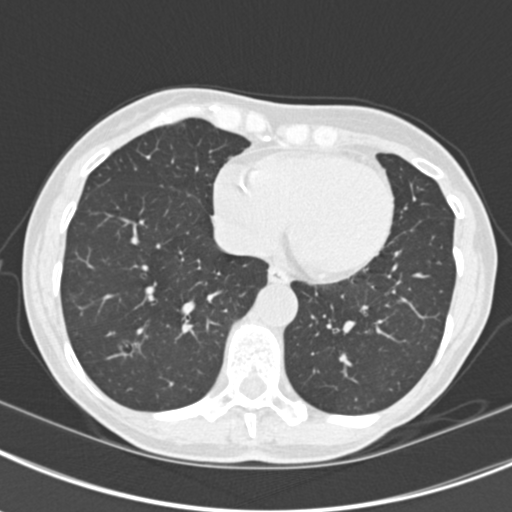
Axial slice from a low-dose chest CT screening exam; second annual screen; lung window (W 1500 / L -600 HU); 2 mm slice thickness; standard (soft-tissue) reconstruction kernel (B30f); 512 × 512 image matrix, field of view 298 × 298 mm. Female participant, aged 63 years at enrolment. Current smoker at enrolment.
Expert-annotated lung lesion, bounding box [x1, y1, x2, y2] px = [109, 327, 152, 369]. The screening reader recorded 9 non-calcified nodules or masses ≥4 mm on this exam (left upper lobe, right upper lobe, left upper lobe, left lower lobe, right middle lobe, left lower lobe, left lower lobe, right lower lobe, right lower lobe); which of them this box marks is not recorded. Official screen result: positive, other. Lung cancer was diagnosed 408 days after this screen (after the third annual screen): bronchiolo-alveolar adenocarcinoma, NOS, right upper lobe, right middle lobe, right lower lobe, left upper lobe, left lower lobe, moderately differentiated (G2), stage IV (AJCC 6th edition).